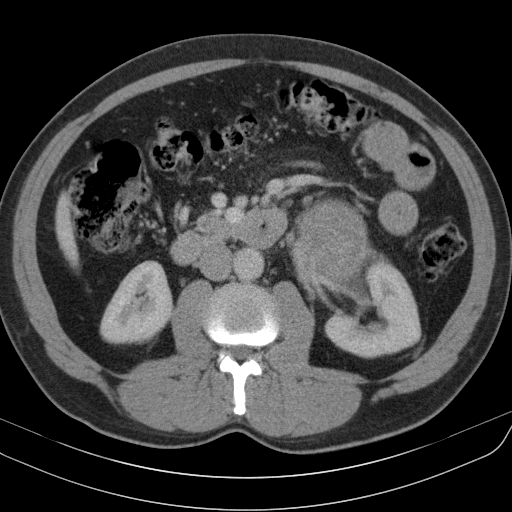
Contrast-enhanced abdominal CT, one axial slice; slice 55 of 91 in the series (ordered by position); reconstruction kernel B31s; 130 kVp; intravenous contrast given; soft-tissue window (W 400 / L 40 HU); 5 mm slice thickness; 512 × 512 image matrix, field of view 370 × 370 mm. Male patient, age 51 years. From the clinical record (not read from this slice): diagnosis: adrenocortical carcinoma; tumour side: left adrenal; tumour size at pathology: 18 cm; Ki-67 index: 40 %; stage (as recorded): 3.
Annotated regions visible in this slice (semi-automatic segmentation, software-assisted and operator-edited):
- mass: bounding box <297,202,364,283> (left, top, right, bottom; pixels)